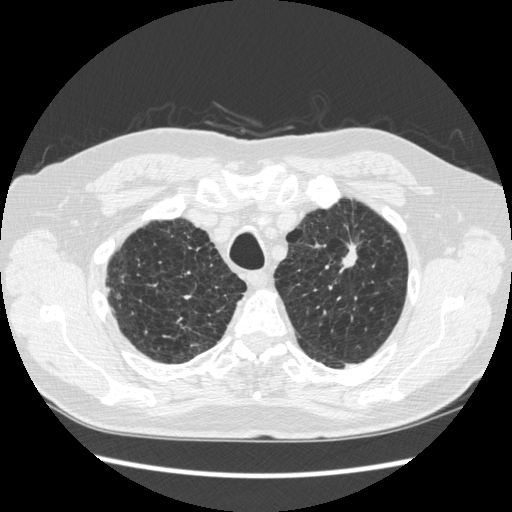
Low-dose screening chest CT, axial slice. Third screening round (two years after baseline). Lung window (W 1500 / L -600 HU). Male, age 70 years at enrolment. Former smoker at enrolment.
Lesion marked by an expert reader, box from (x=323, y=220) to (x=375, y=285) px. The screening reader recorded 2 non-calcified nodules or masses ≥4 mm on this exam; which of them this box marks is not recorded. Participant outcome: lung cancer diagnosed 92 days after this screen — squamous cell carcinoma, NOS, left upper lobe, moderately differentiated (G2), stage IA (AJCC 6th edition), 18 mm at pathology.